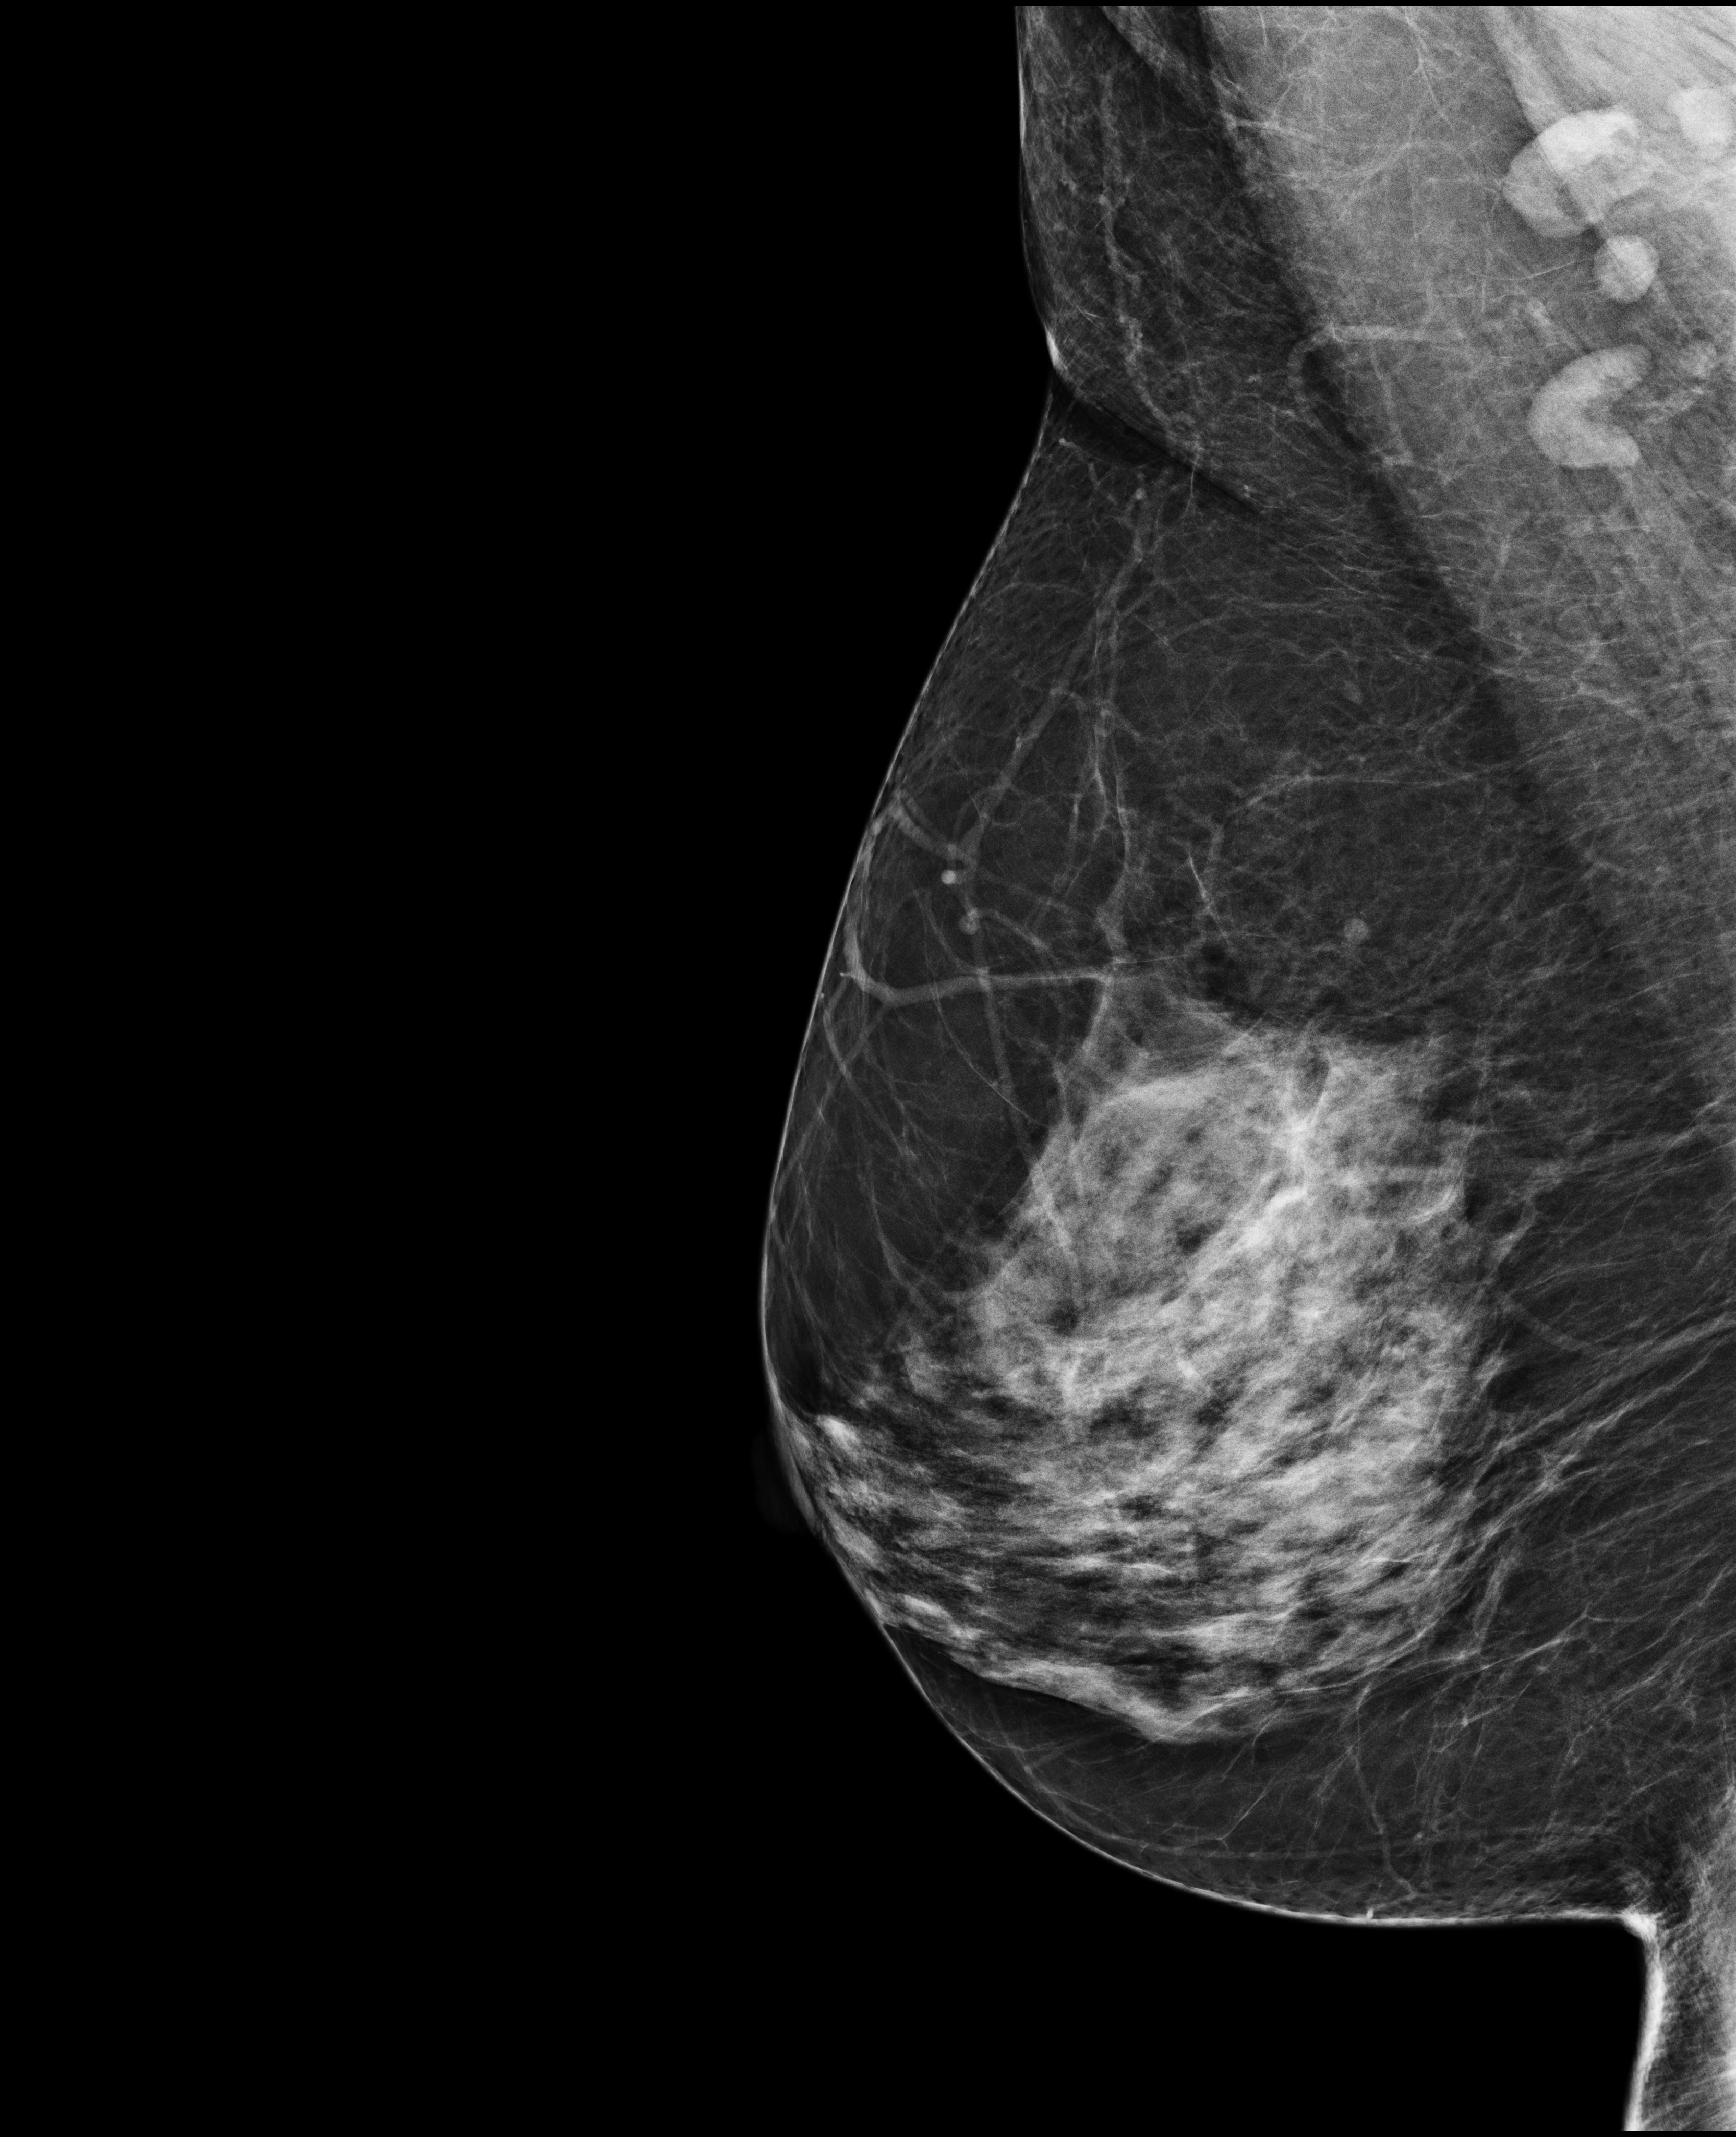
Digital mammogram (FFDM); right breast; MLO view; annual screening mammography examination; compressed breast thickness 74 mm. Patient aged 59 years (female).
BI-RADS breast density category at the screening exam (both breasts, scale 1–4): 3. Final BI-RADS assessment for this screening round (tomosynthesis exam, both breasts): category 2. Recall: no recall after this screen.